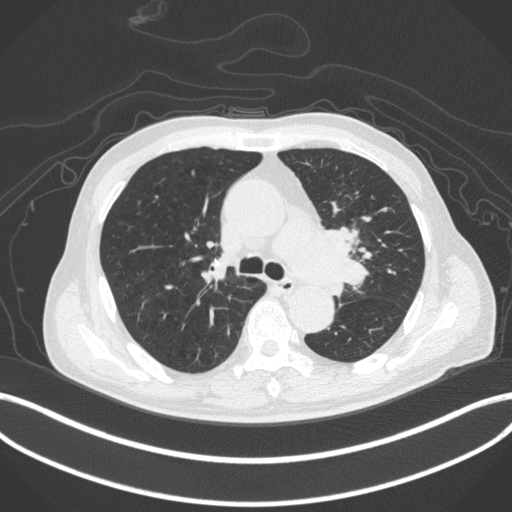
Chest CT, one axial slice. Reconstruction kernel B31f. 120 kVp. Lung window (W 1500 / L -600 HU). 1 mm slice thickness. 512 × 512 image matrix, field of view 400 × 400 mm. Patient: male, 77 years. Case-level facts recorded for this patient, not image findings: clinical TNM (as recorded): T3 N1 M0.
Structures marked on this image (bounding box drawn by a radiologist):
- lung tumour (recorded histology: adenocarcinoma): bounding box [x1, y1, x2, y2] px = [314, 225, 371, 294]